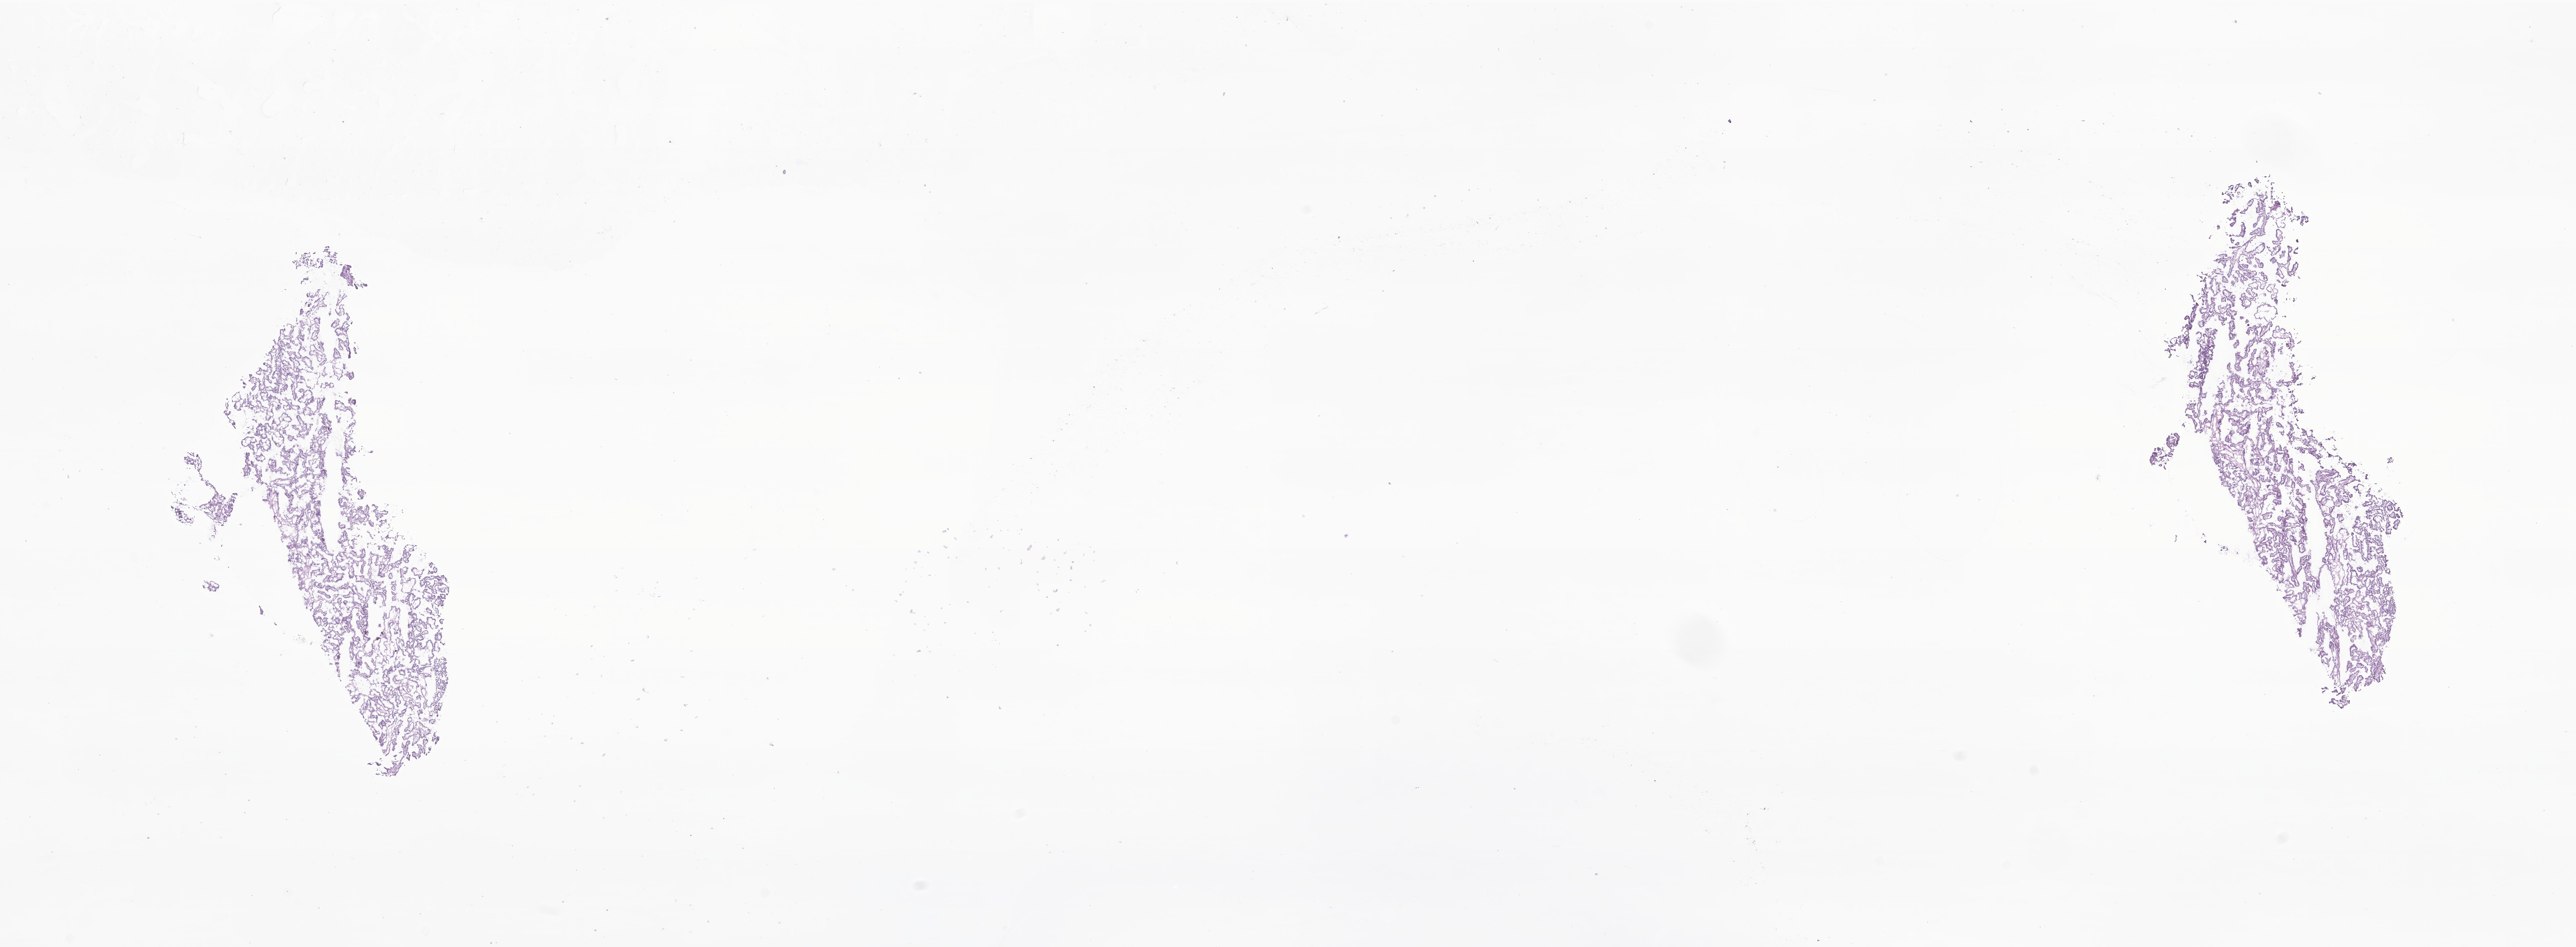
Digitized hematoxylin and eosin (H&E)-stained section of tumor tissue from the brain, whole scanned area (about 27.4 x 10.1 mm) shown as a low-resolution overview, cryosection (OCT / tissue freezing medium). Patient female; age 54 months (4 years 6 months).
Recorded diagnosis: Neoplasm, uncertain whether benign or malignant.